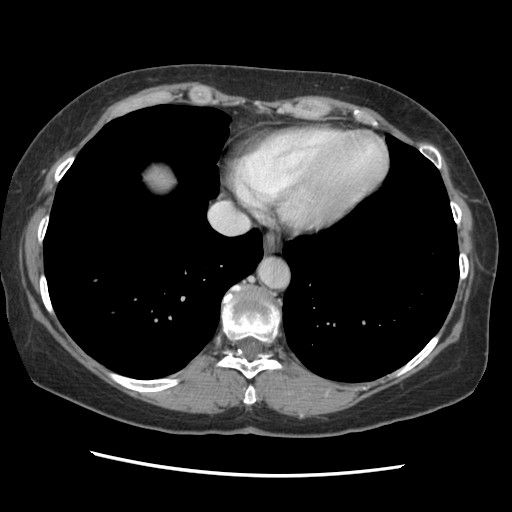
Contrast-enhanced abdominal CT, one axial slice. Slice 128 of 141 in the series (ordered by position). Soft-tissue window (W 400 / L 40 HU). 2.5 mm slice thickness. 512 × 512 image matrix, field of view 330 × 330 mm. Female patient, age 61 years. From the clinical record (not read from this slice): diagnosis: colorectal cancer liver metastases, imaged before liver resection; multiple liver metastases: no; largest metastasis: 2.4 cm; disease in both lobes: no.
Annotated regions visible in this slice (expert manual segmentation):
- liver: bounding box (x1, y1, x2, y2) in pixels: (146, 164, 173, 194)
- planned liver remnant (the part of the liver to remain after resection): (146, 164, 173, 194)